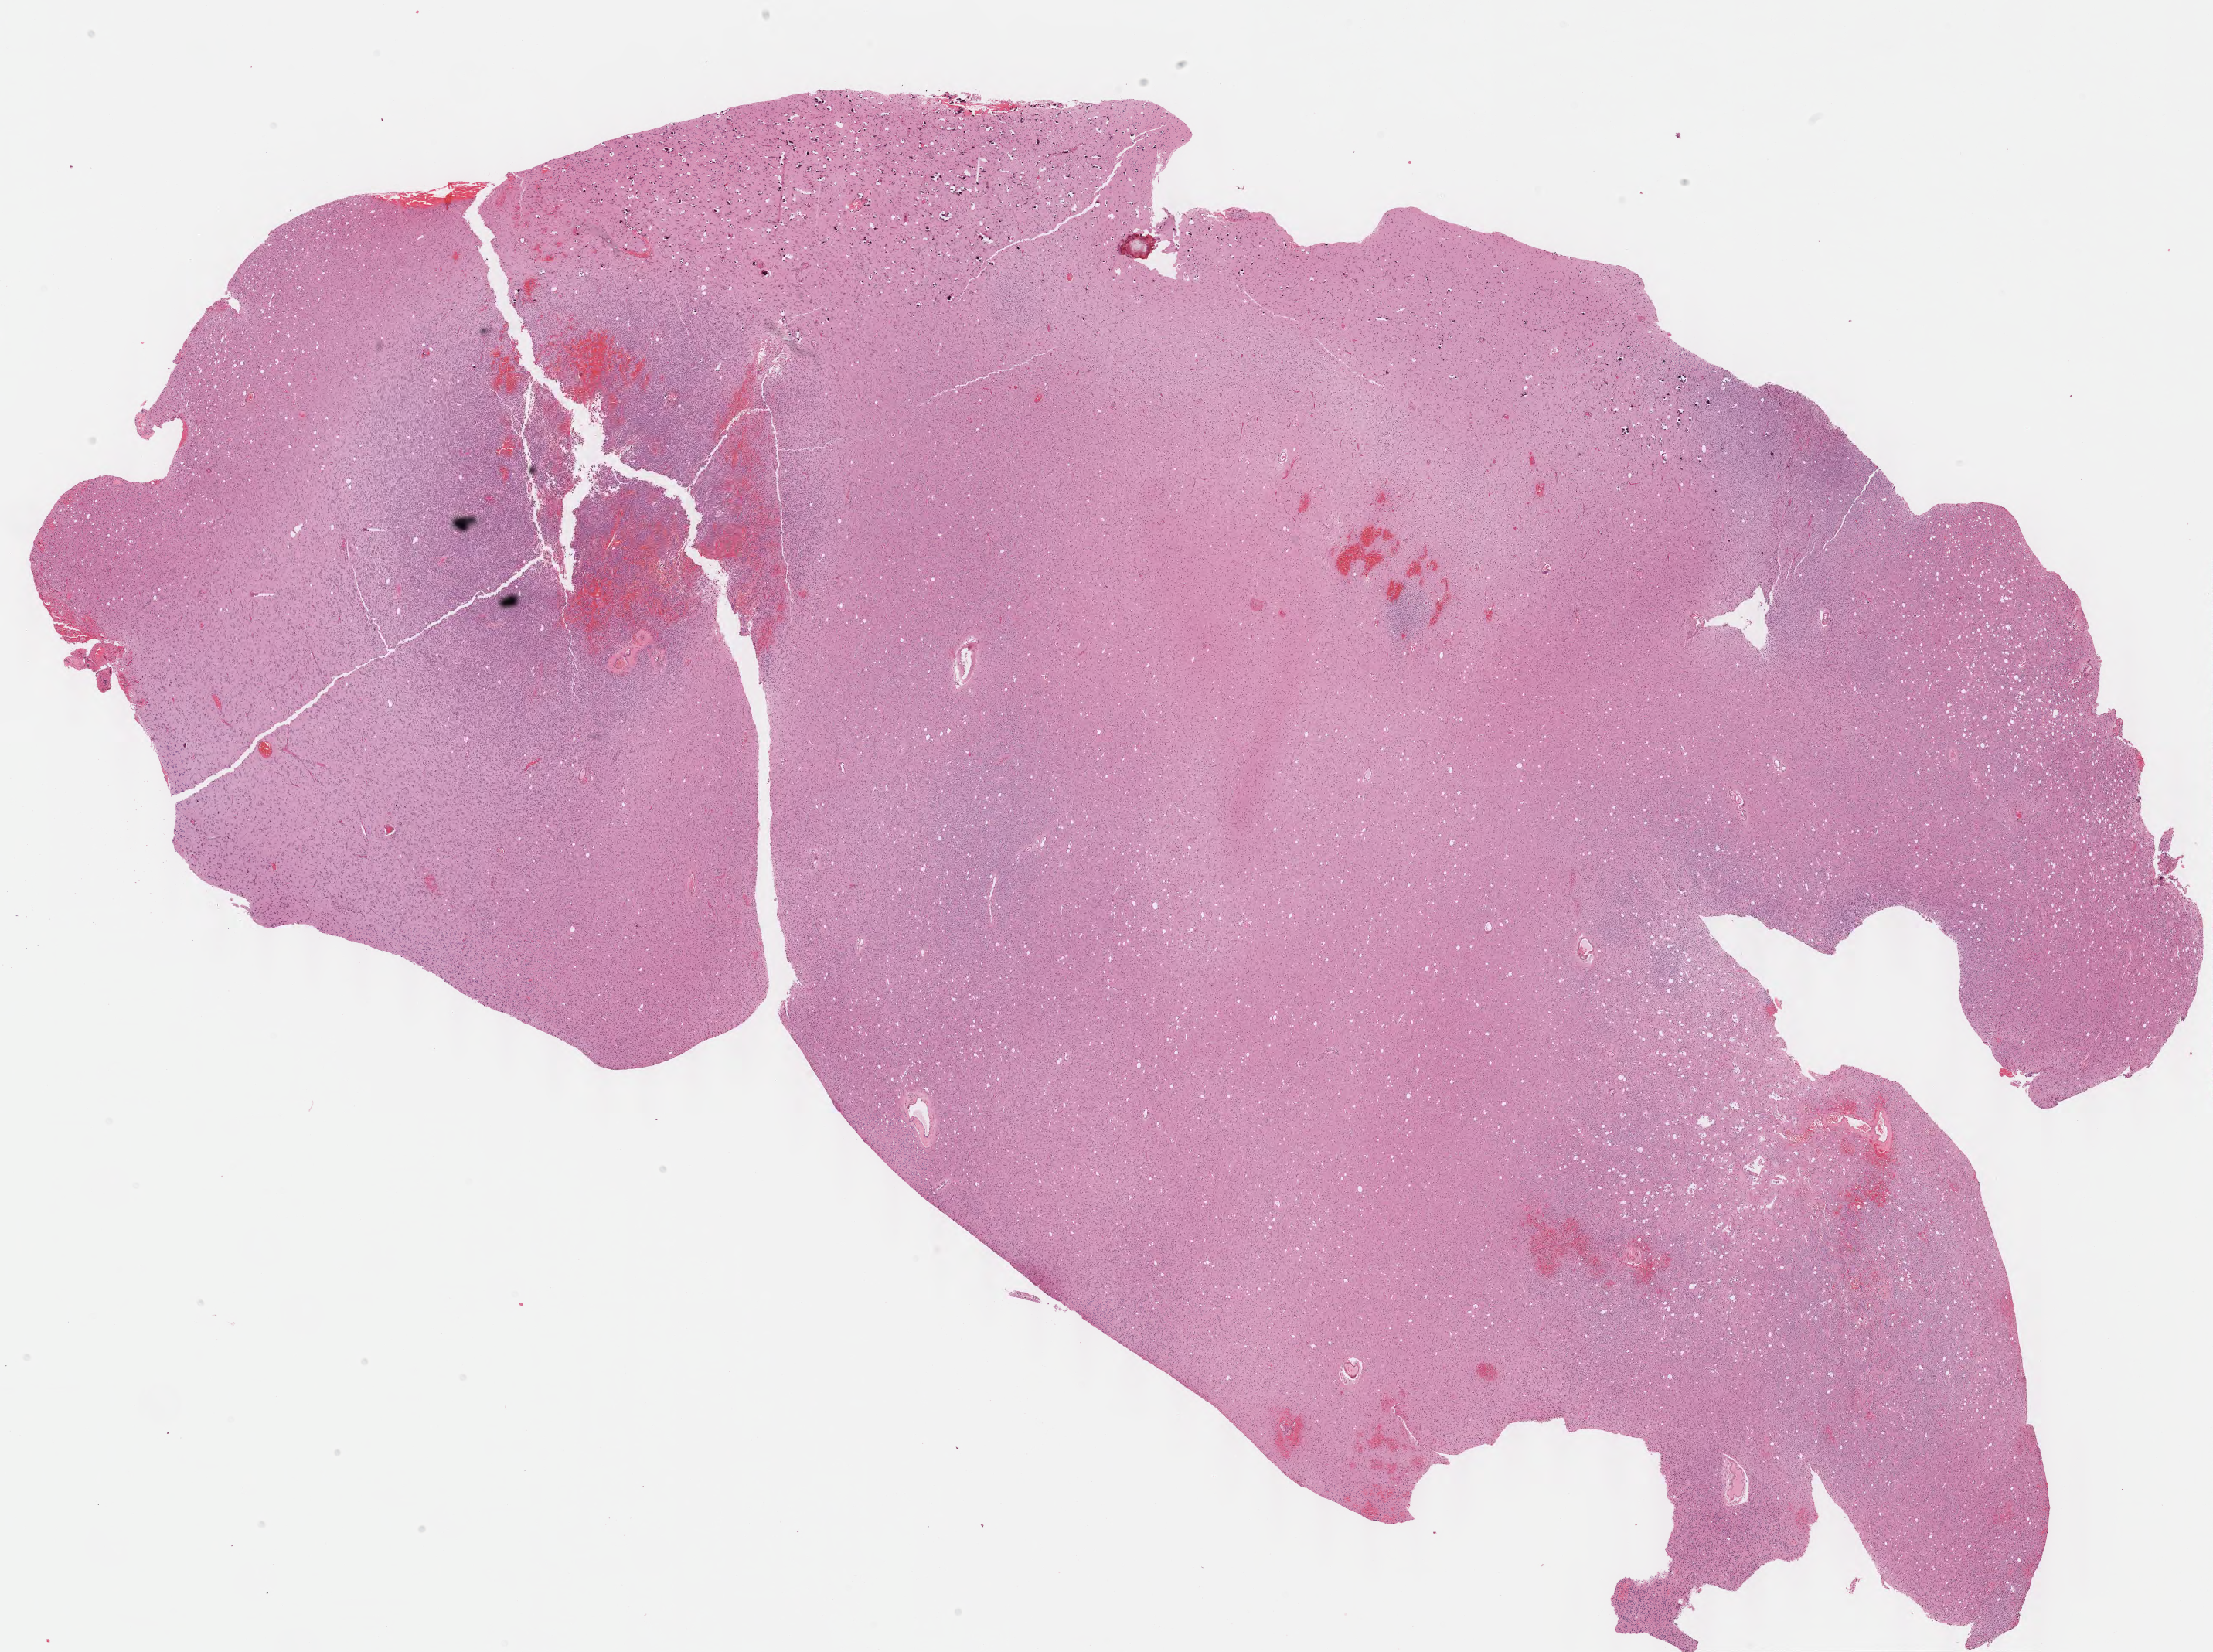
Digitized H&E-stained tissue section (whole slide), a low-resolution overview of the entire scanned area, about 22.6 x 16.9 mm, FFPE section, brain, primary tumour sample. Male, age 40 years at initial diagnosis. Histologic grade: G3 (poorly differentiated).
* diagnosis: Oligodendroglioma, anaplastic